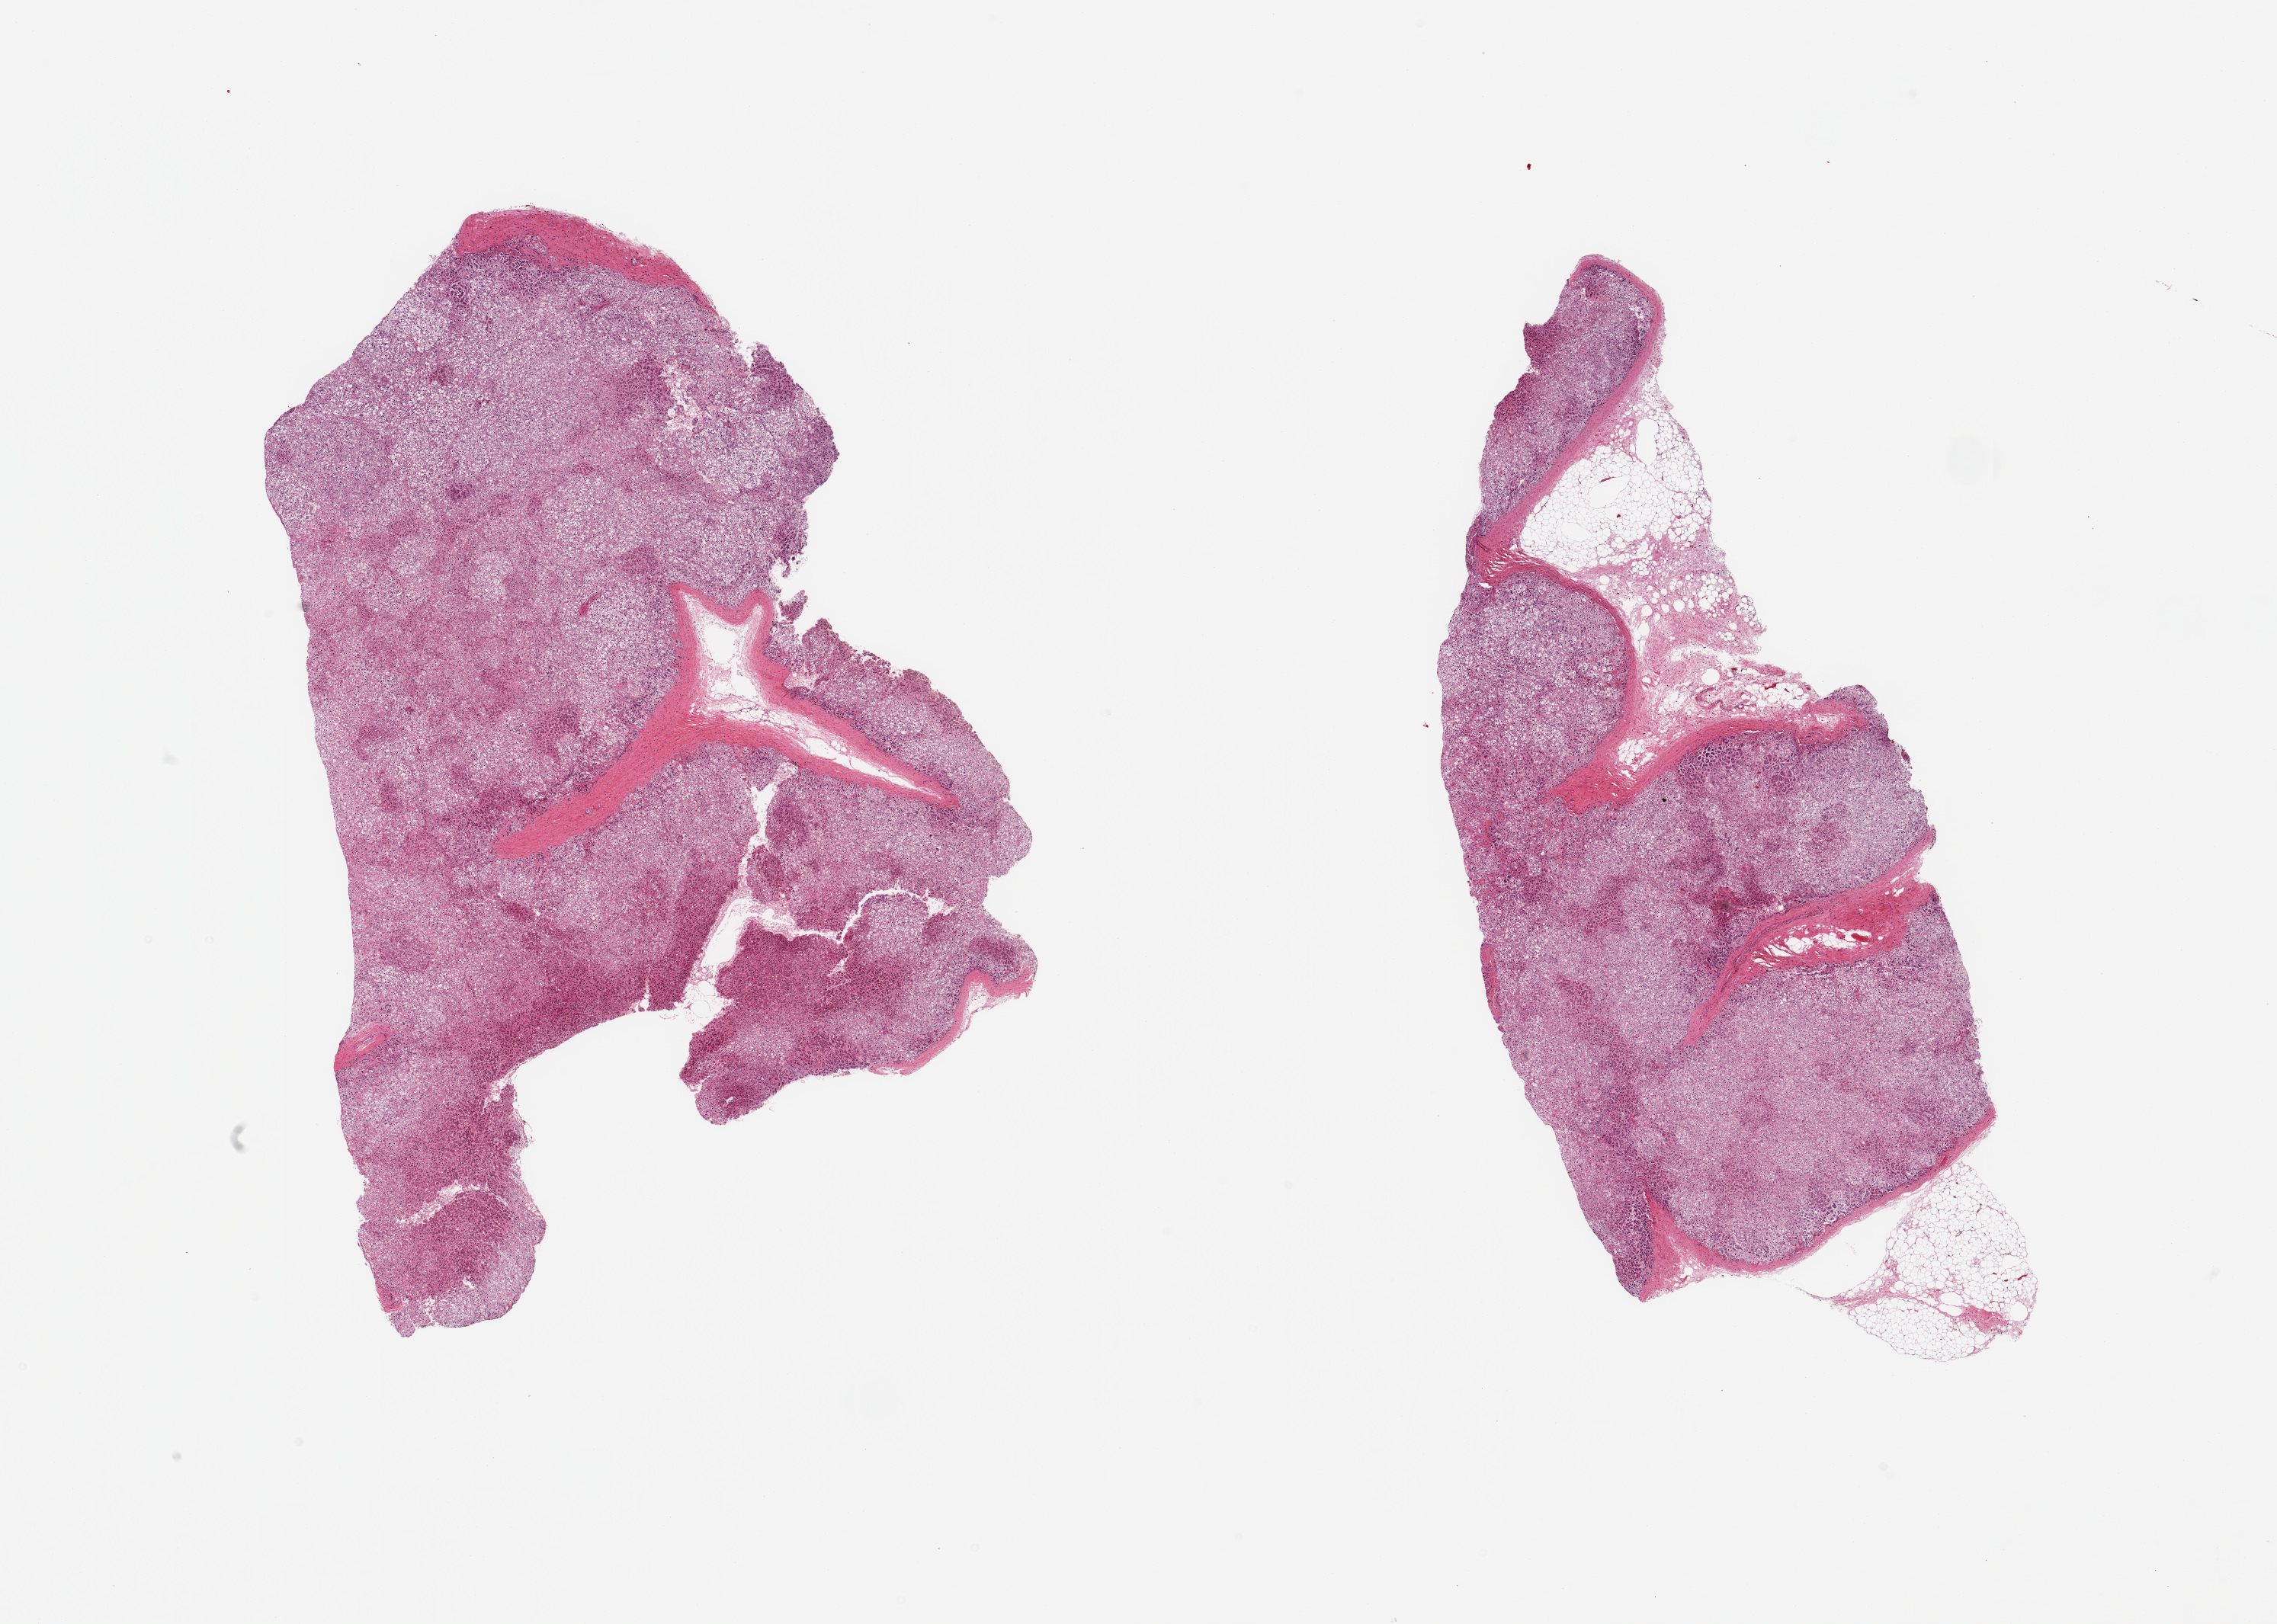
H&E whole-slide image — whole scanned area (about 23.6 x 16.9 mm, slide scanned at 20x) shown as a low-resolution overview; PAXgene-fixed, paraffin-embedded tissue; section of adrenal gland (target tissue); donor tissue sample. Female donor.
* pathologist's review note for this sample: 2 pieces: 1 well trimmed, other with 20% external fat